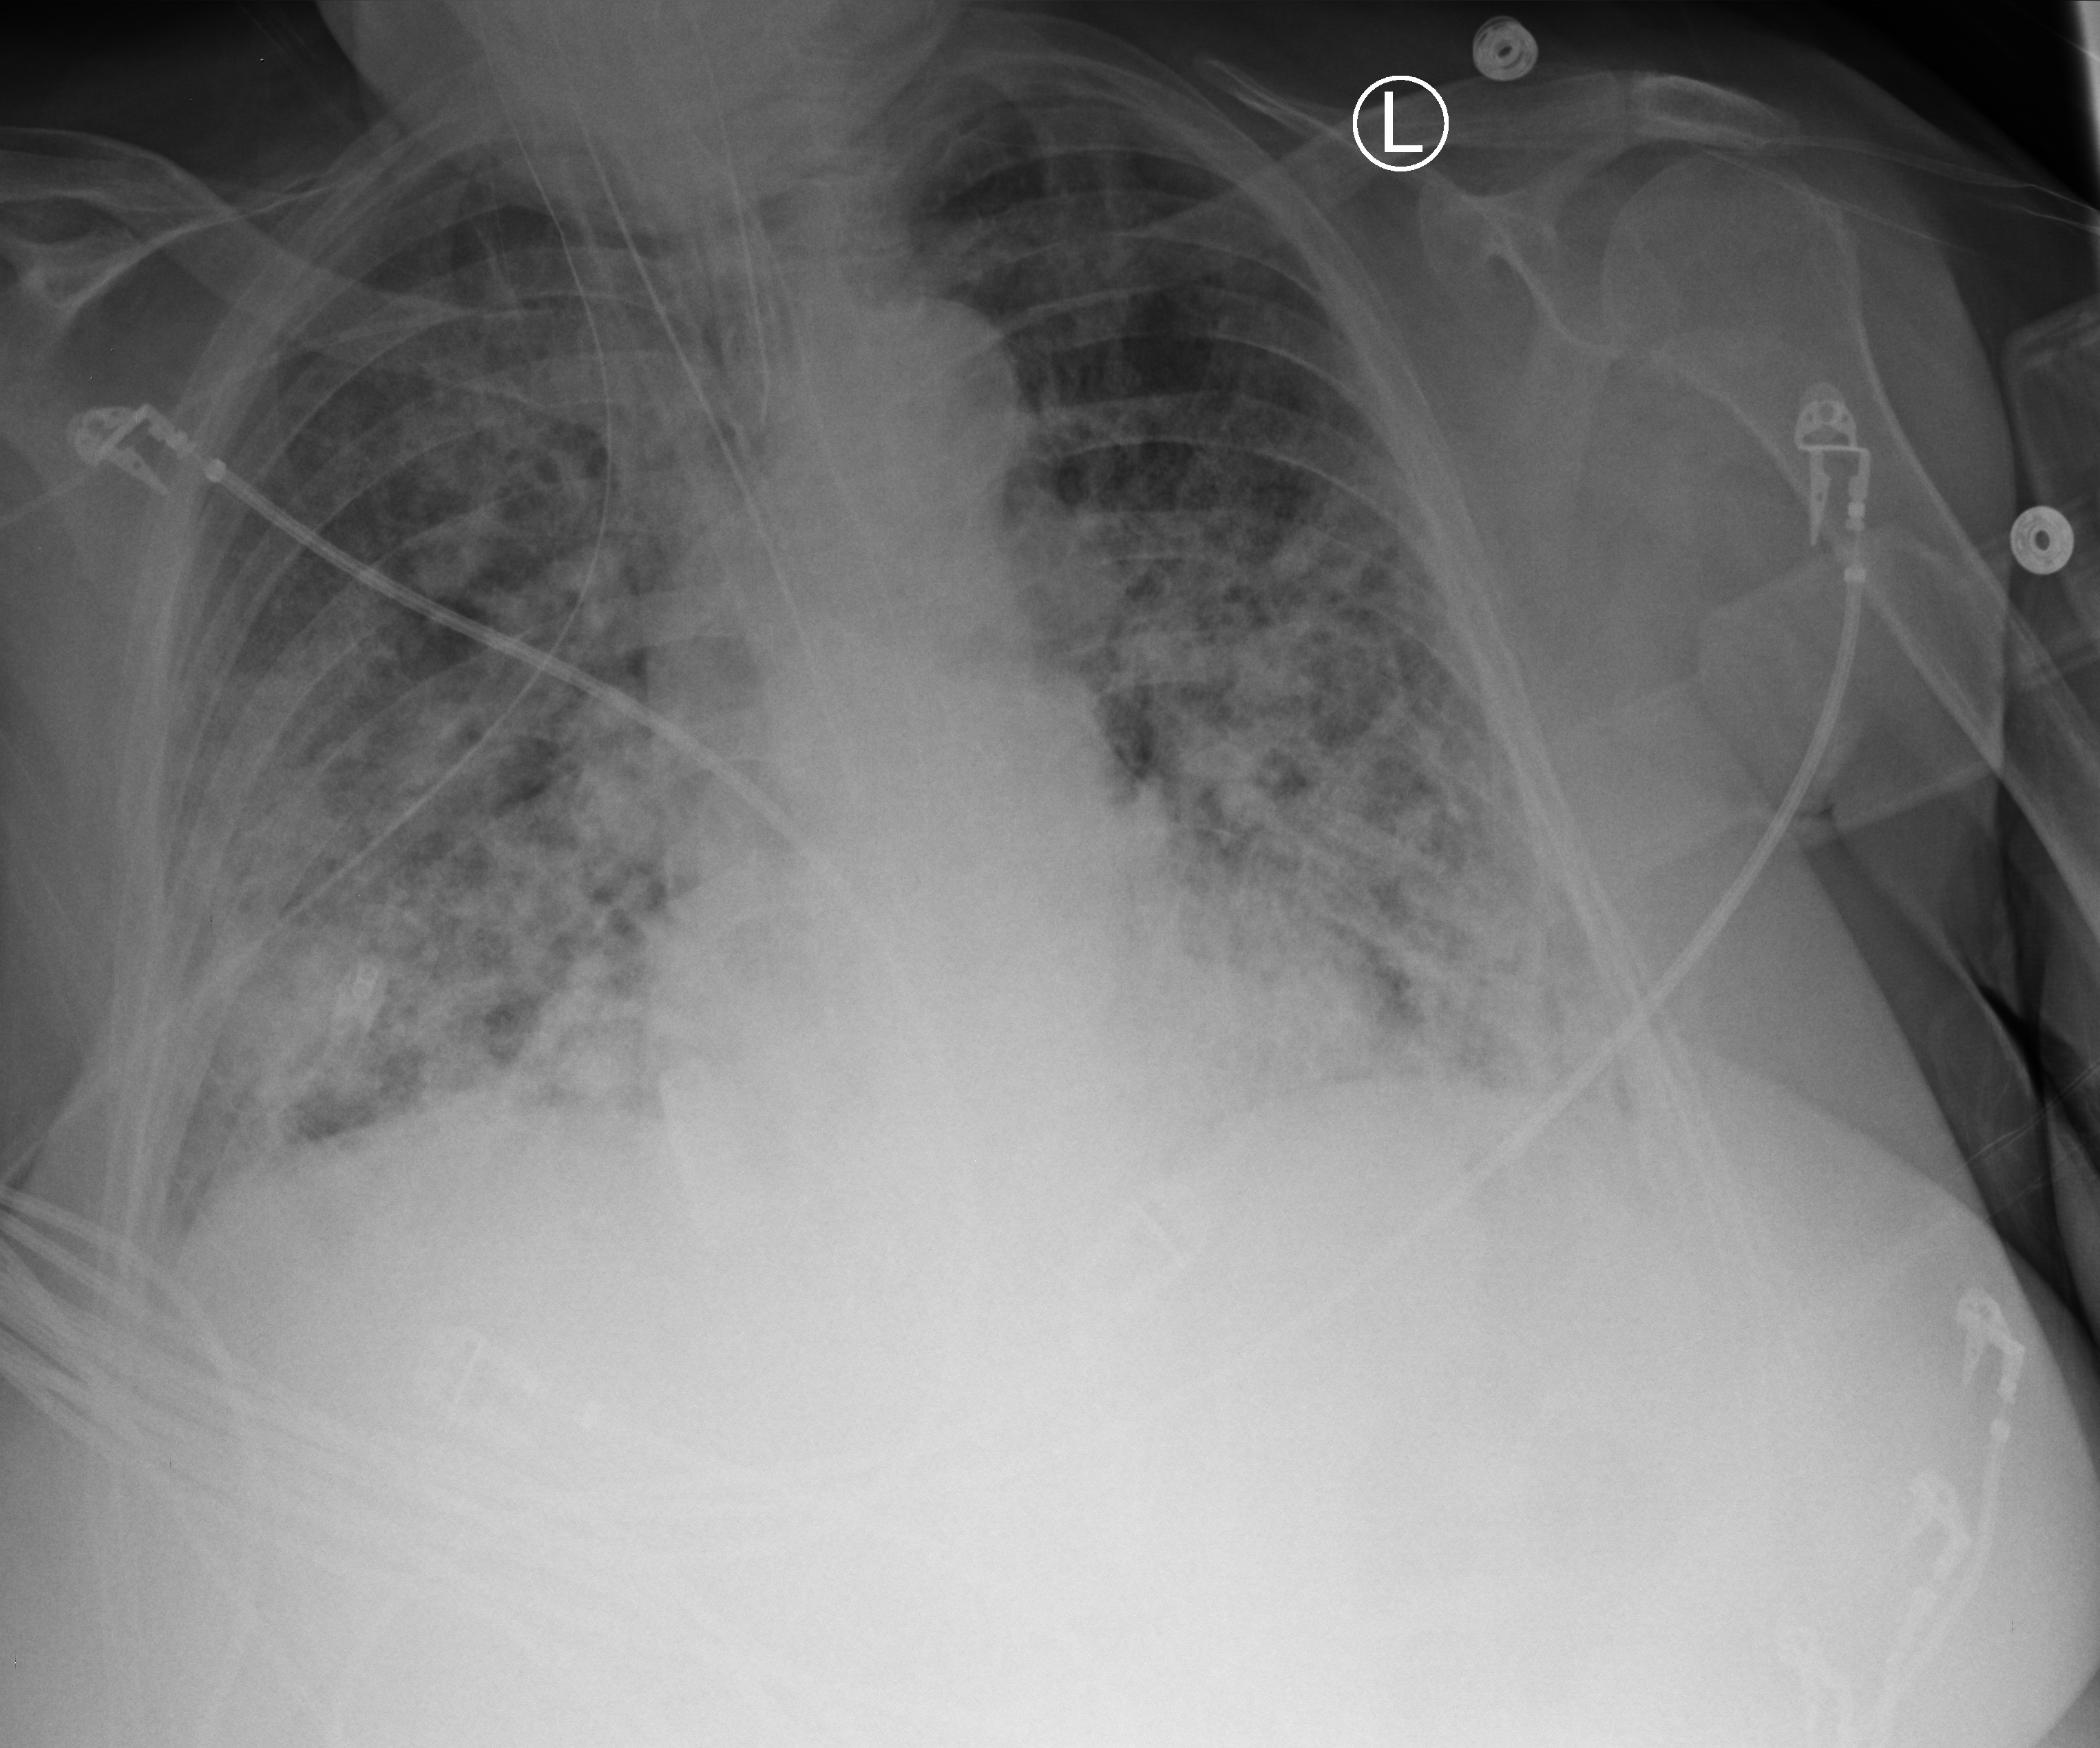
Portable chest radiograph; anteroposterior (AP) projection. Female patient hospitalised with COVID-19, age 60–74 years.
Hospital-stay facts (about this admission, not read from this image; timing relative to this image not recorded):
- COPD (admission record): no
- length of hospital stay: 19 days
- mechanically ventilated during this hospital stay: yes